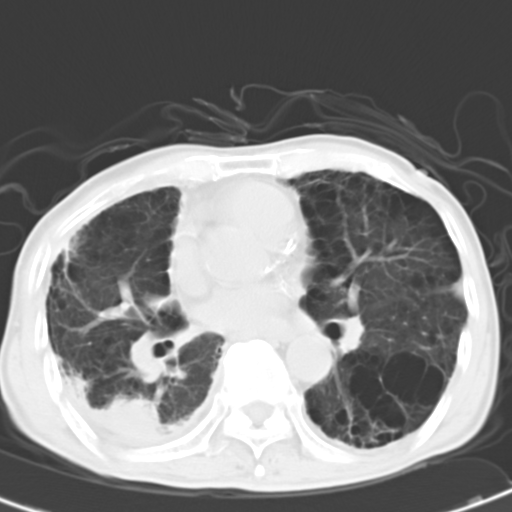
Chest CT, one axial slice. Slice 14 of 31 in the series (ordered by position). Reconstruction kernel B40f. Lung window (W 1500 / L -600 HU). 512 × 512 image matrix. Male patient, age 67 years. Case-level facts recorded for this patient, not image findings: clinical TNM (as recorded): T2 N3 M1.
Structures marked on this image (rectangle marked by the reading radiologist):
- lung tumour (recorded histology: adenocarcinoma): bounding box [x1, y1, x2, y2] px = [98, 388, 169, 452]